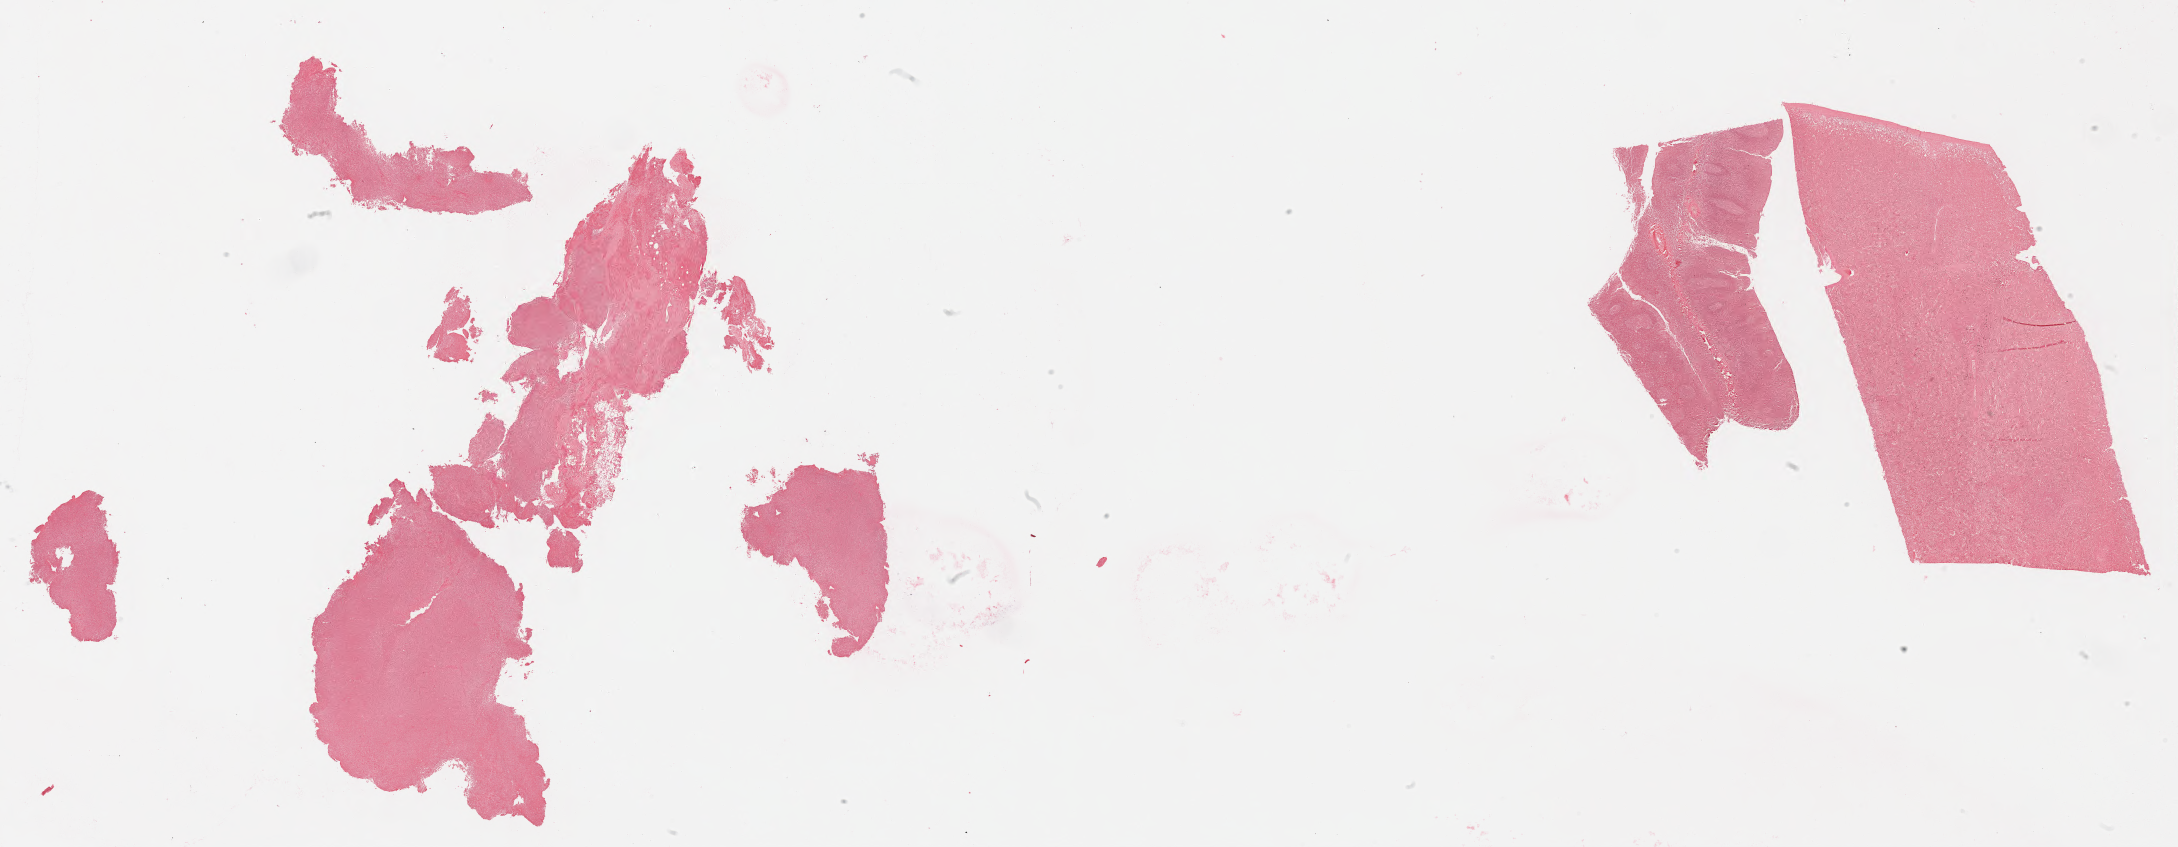
Whole-slide image, Epstein–Barr virus-encoded RNA (EBER) in-situ hybridisation, low-resolution overview of the scanned area, about 35.2 x 13.7 mm, specimen: tumor tissue, site: liver. Patient: female, age 36 years.
Diagnosis: Diffuse large B-cell lymphoma, NOS.